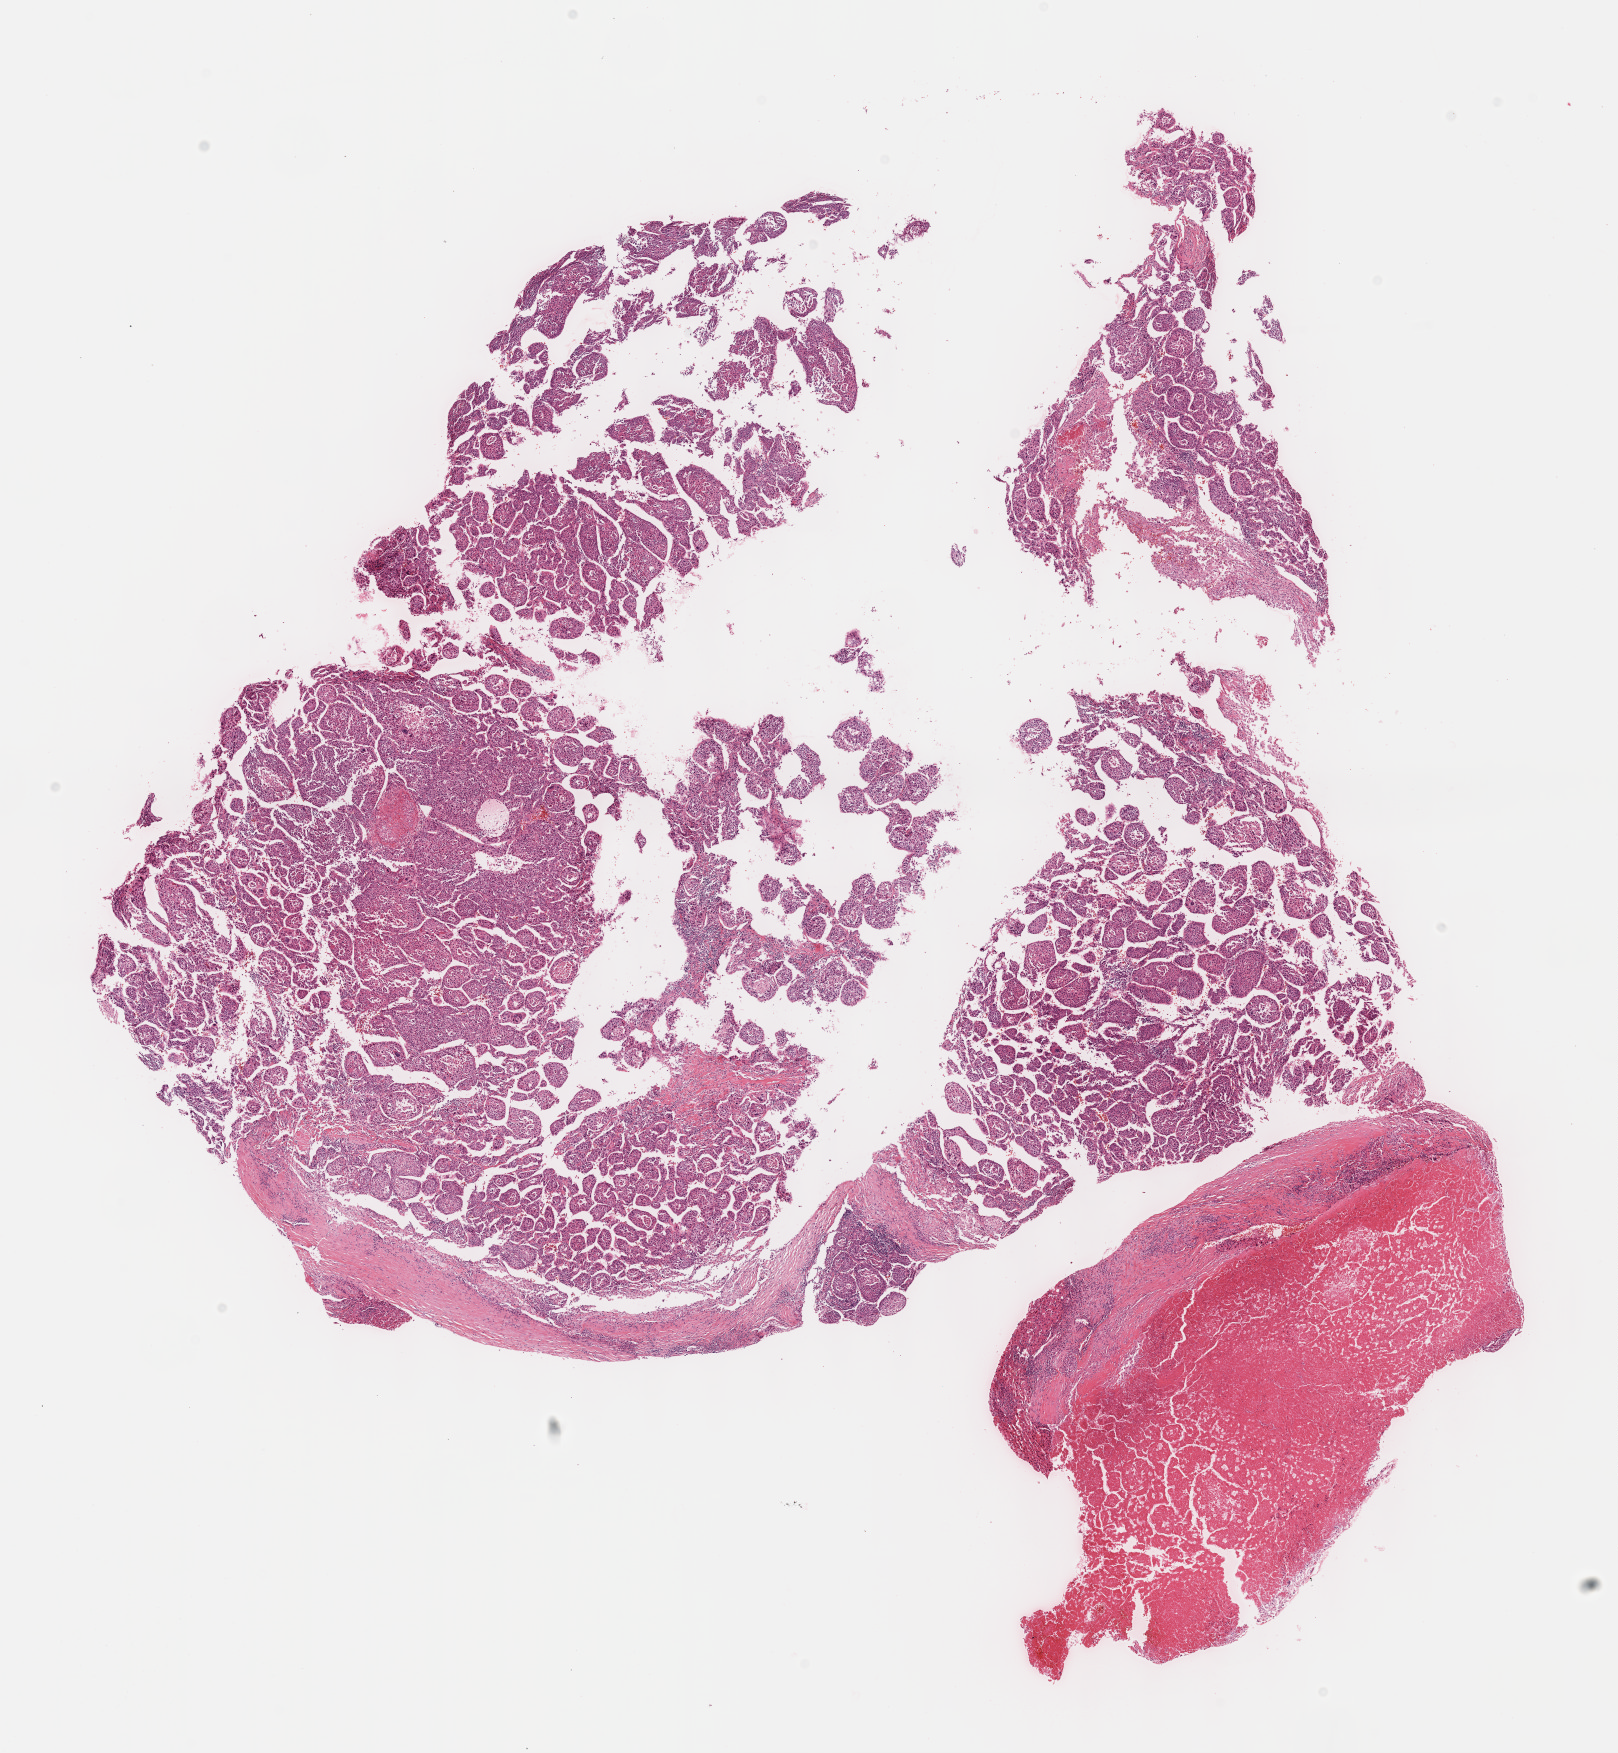
Digitized H&E tissue section (whole slide) — shown as a low-resolution overview of the whole scanned area (about 13.1 x 14.2 mm). Formalin-fixed paraffin-embedded (FFPE) diagnostic section. Sample: primary tumour, liver. Patient: male, age at initial diagnosis 51 years. Histologic grade: G4 (undifferentiated).
* AJCC pathologic stage: I (7th edition)
* histologic diagnosis: Hepatocellular carcinoma, NOS